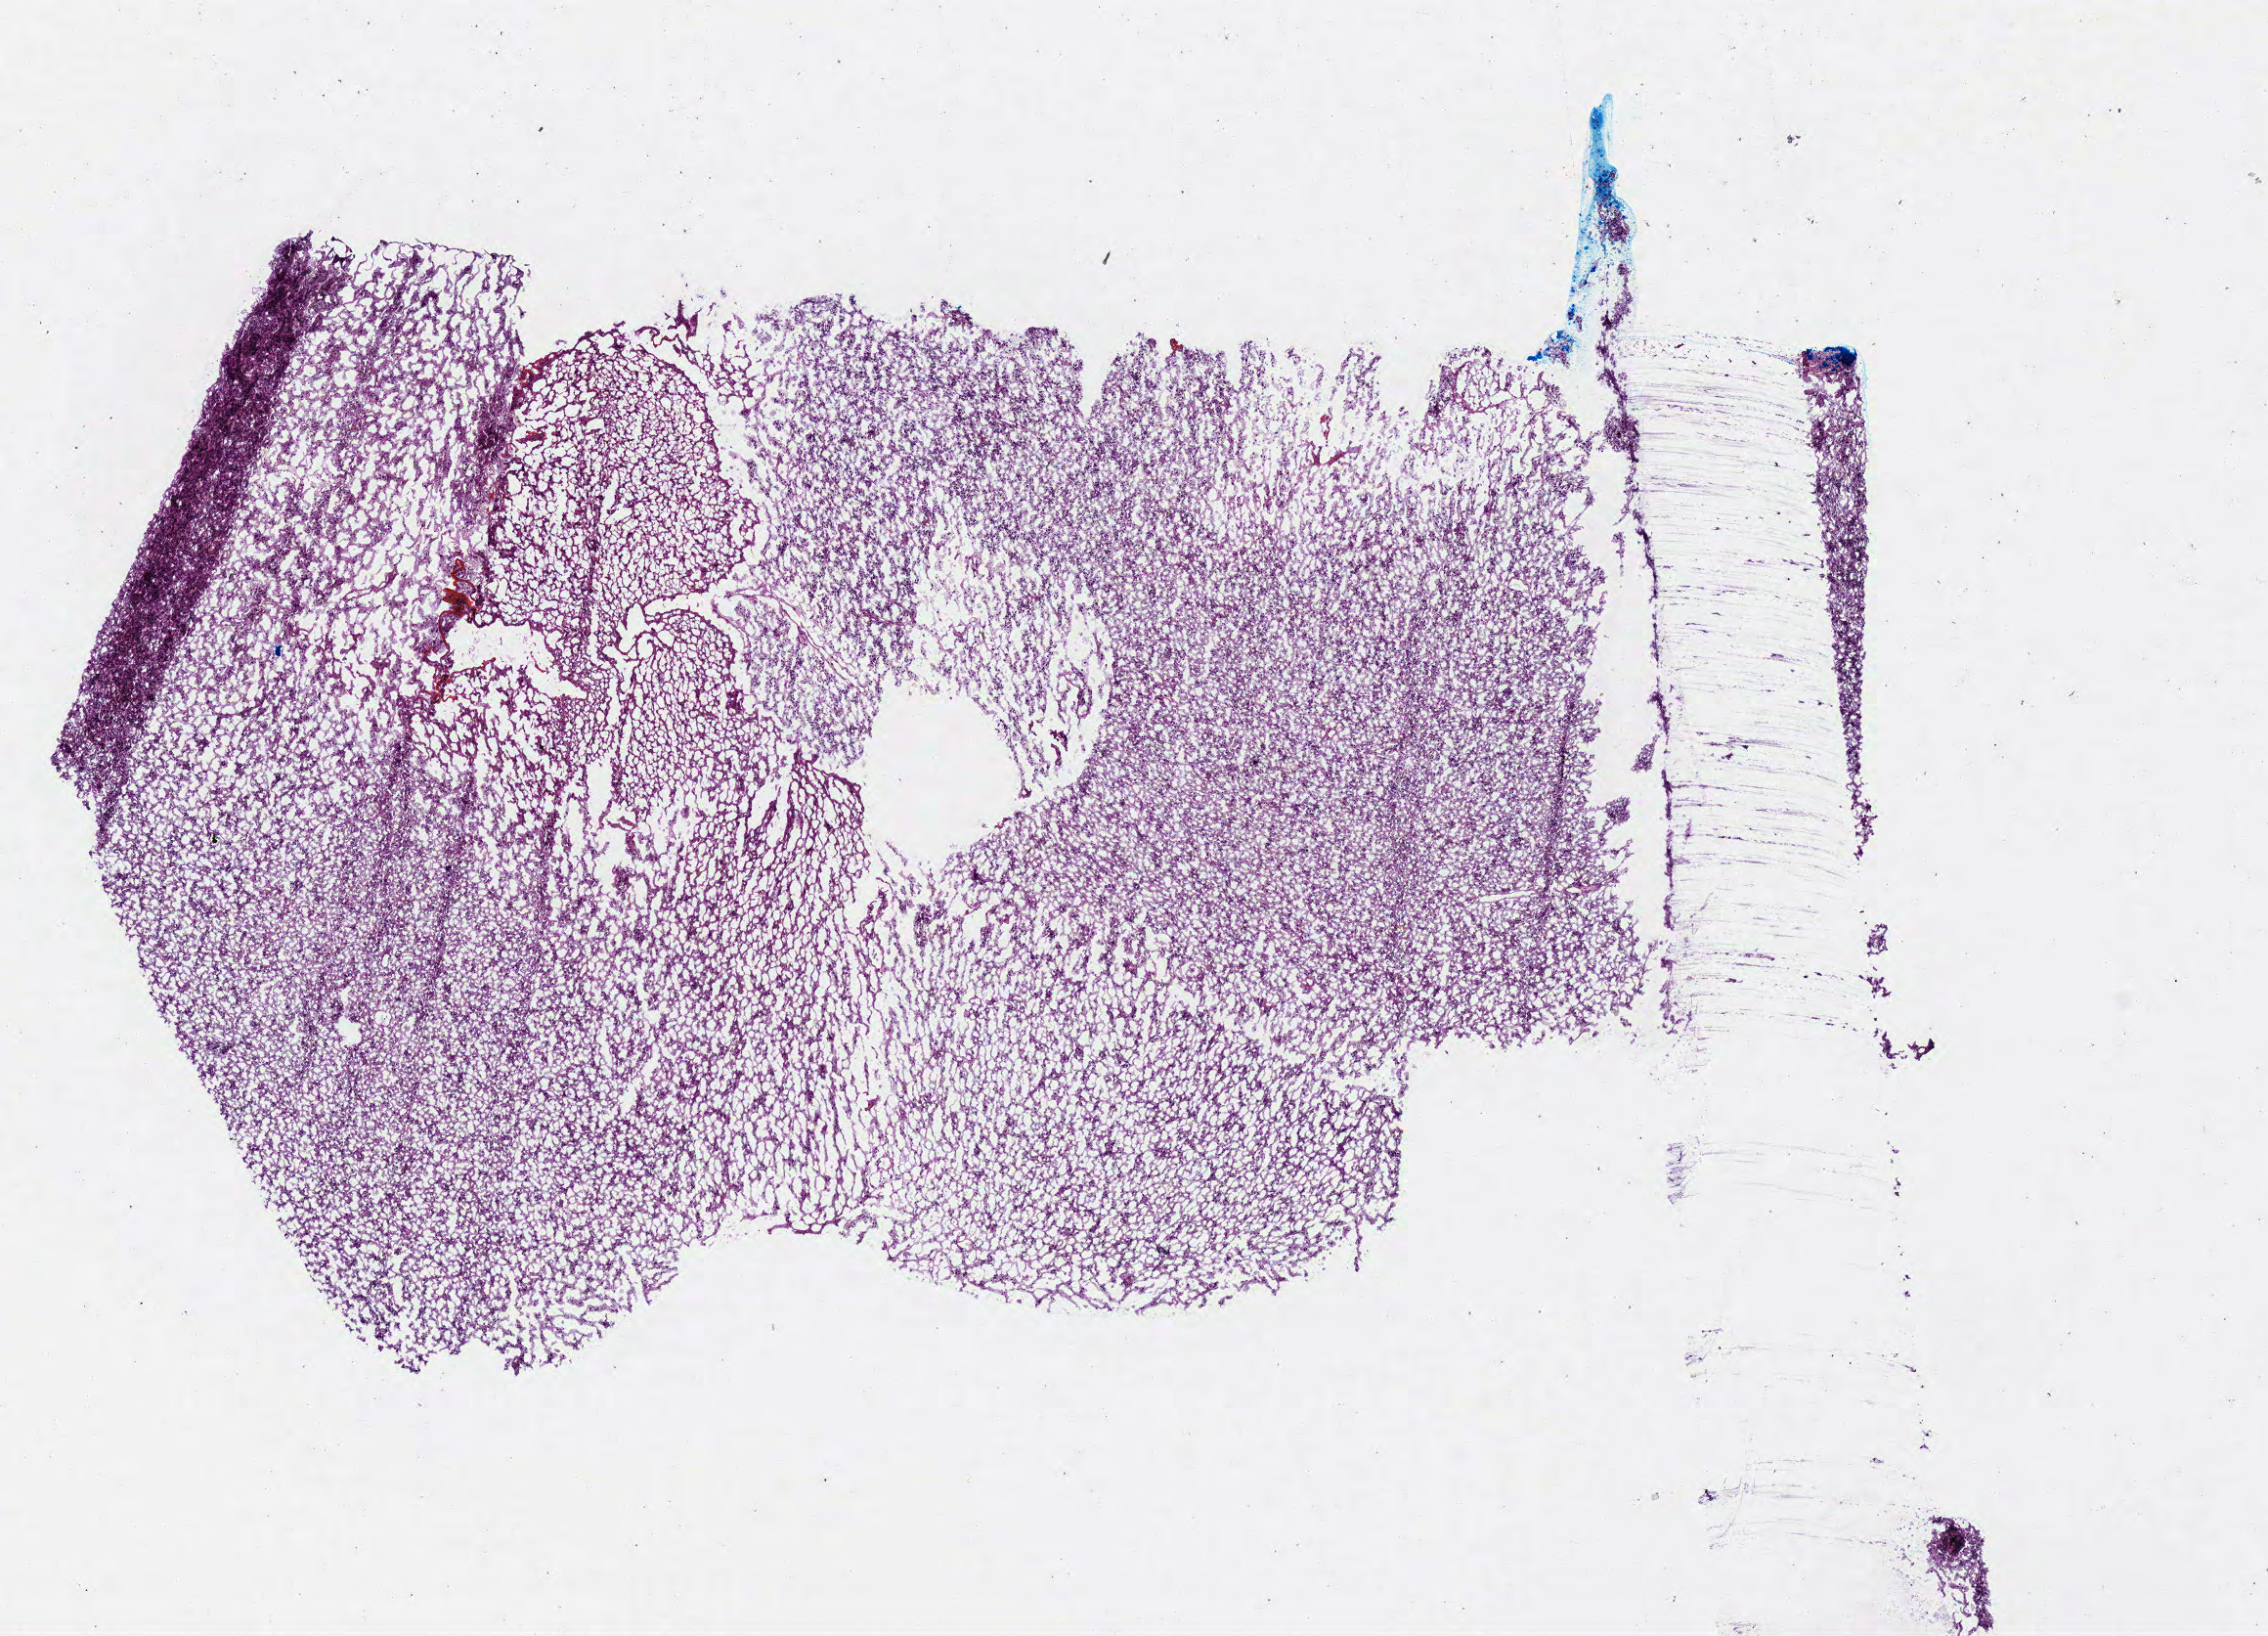
Digitized H&E-stained tissue section (whole slide) — whole scanned area (about 9.1 x 6.6 mm) shown as a low-resolution overview; frozen section; sample: primary tumour, brain. Female, age 52 years at initial diagnosis. Slide review estimates, as recorded: tumour cells 95%, tumour nuclei 75%, normal cells 0%, stromal cells 0%, necrosis 5%.
• diagnosis: Glioblastoma